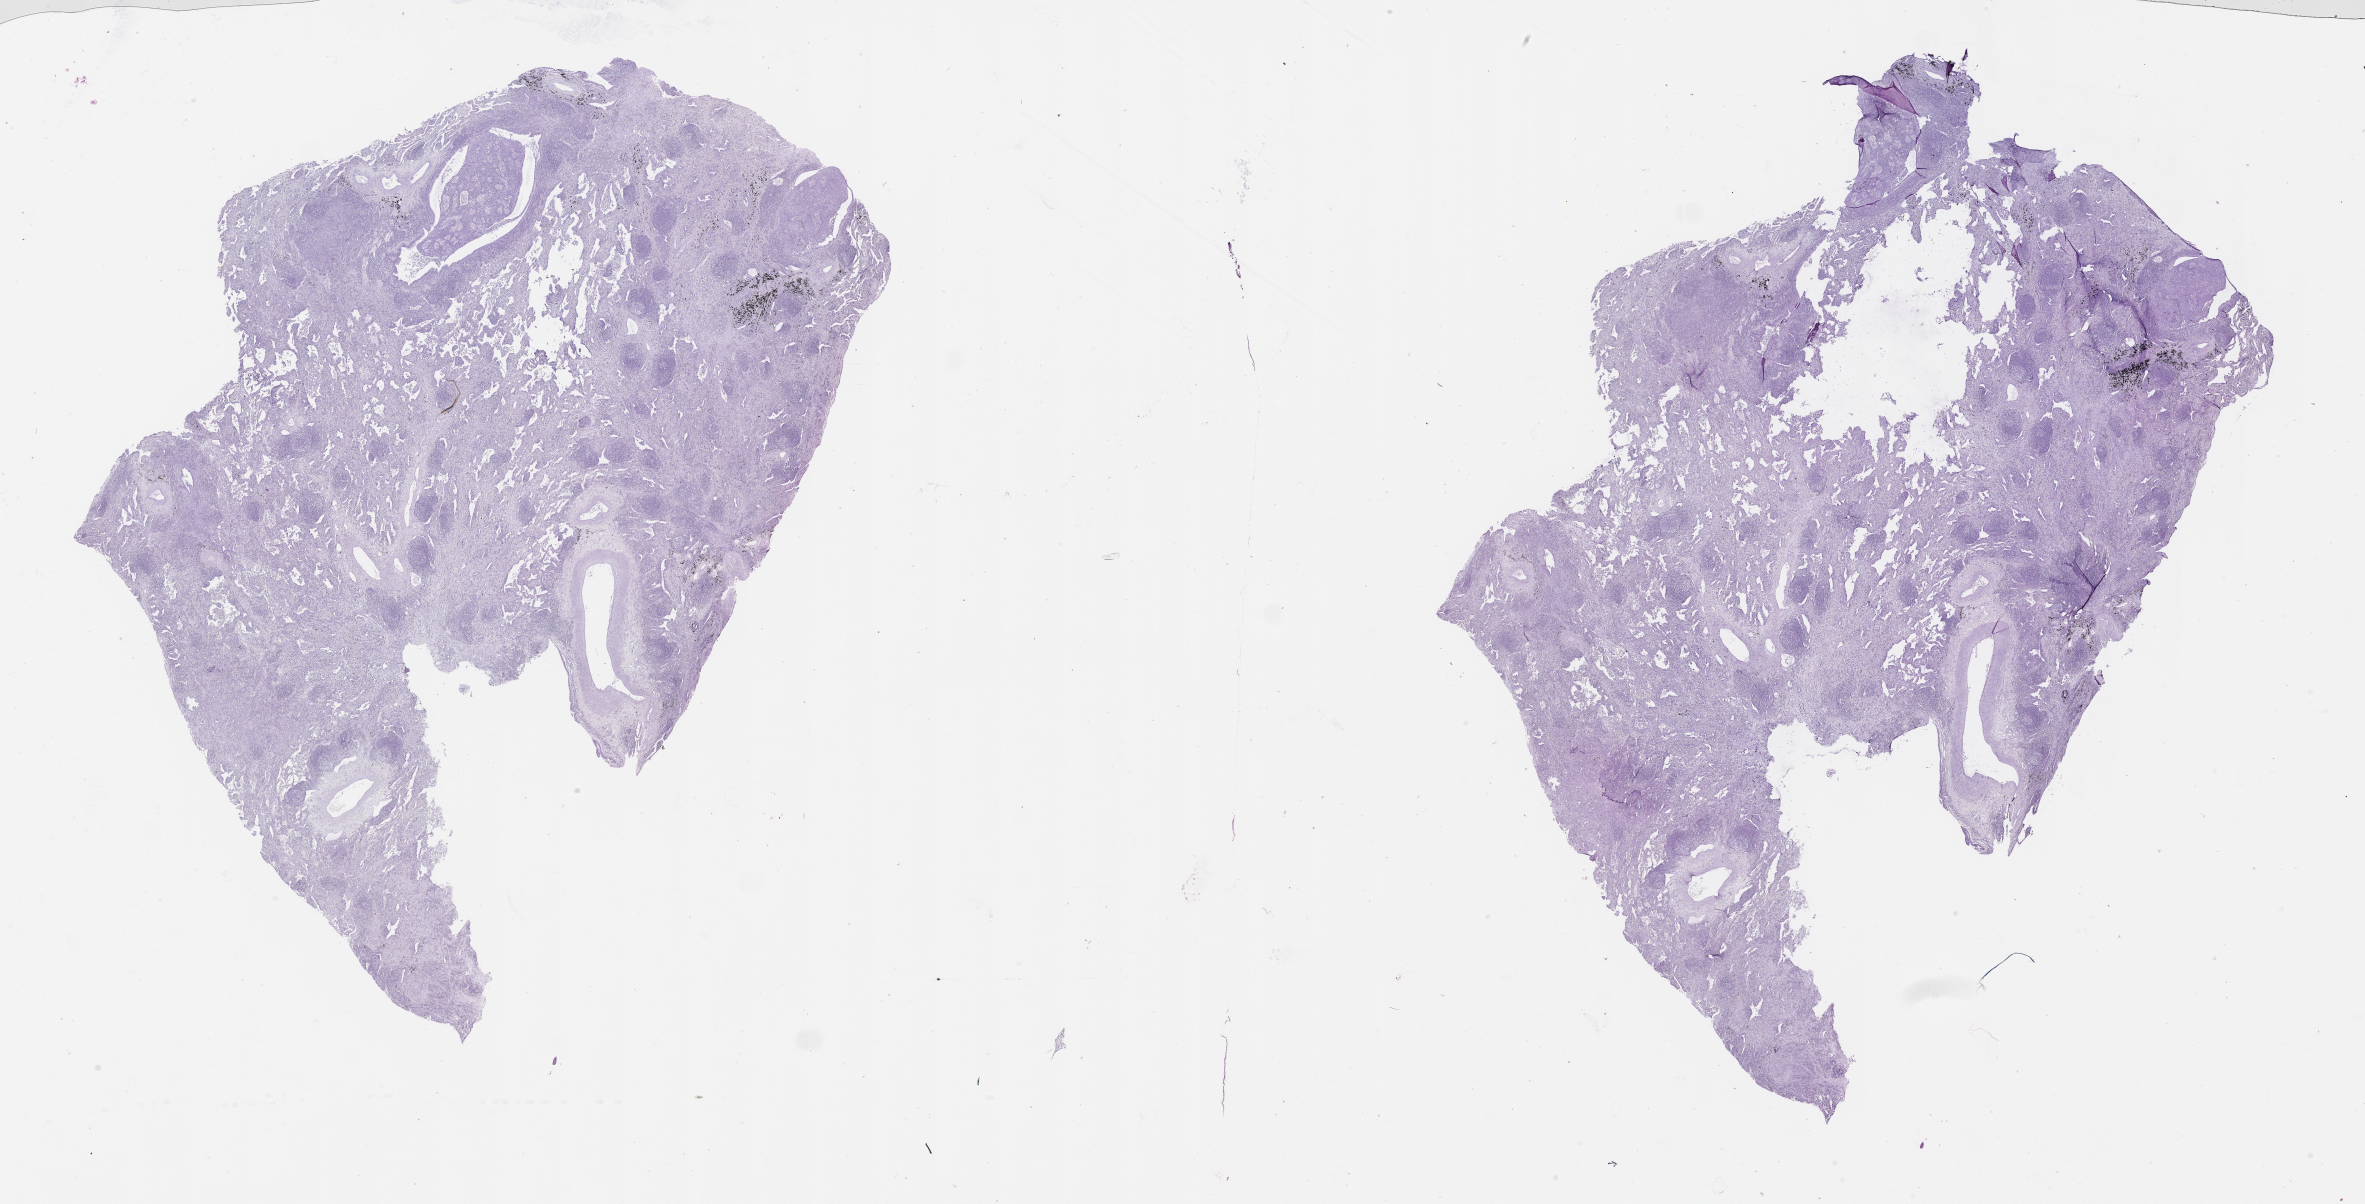
Digitized H&E tissue section (whole slide), low-resolution overview of the scanned area, about 38.1 x 19.4 mm (acquisition: 20x scan), tumour tissue sample, lung. Male, 70 y/o.
Patient diagnosis (cohort enrolment): squamous cell carcinoma (lung).